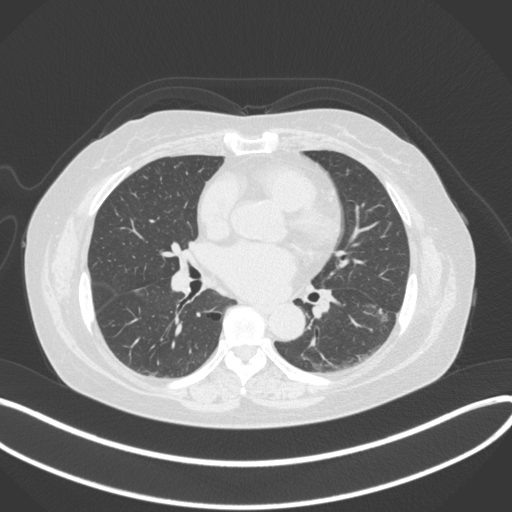
Chest CT, one axial slice; position 178 of 373 along the scan axis; 120 kVp; lung window (W 1500 / L -600 HU); 1 mm slice thickness; 512 × 512 image matrix. Patient: female, 67 years. From the clinical record (not read from this slice): clinical TNM (as recorded): T1c N0 M0.
Annotated regions visible in this slice (rectangle marked by the reading radiologist):
- lung tumour (recorded histology: adenocarcinoma): box from (x=368, y=302) to (x=395, y=325) px